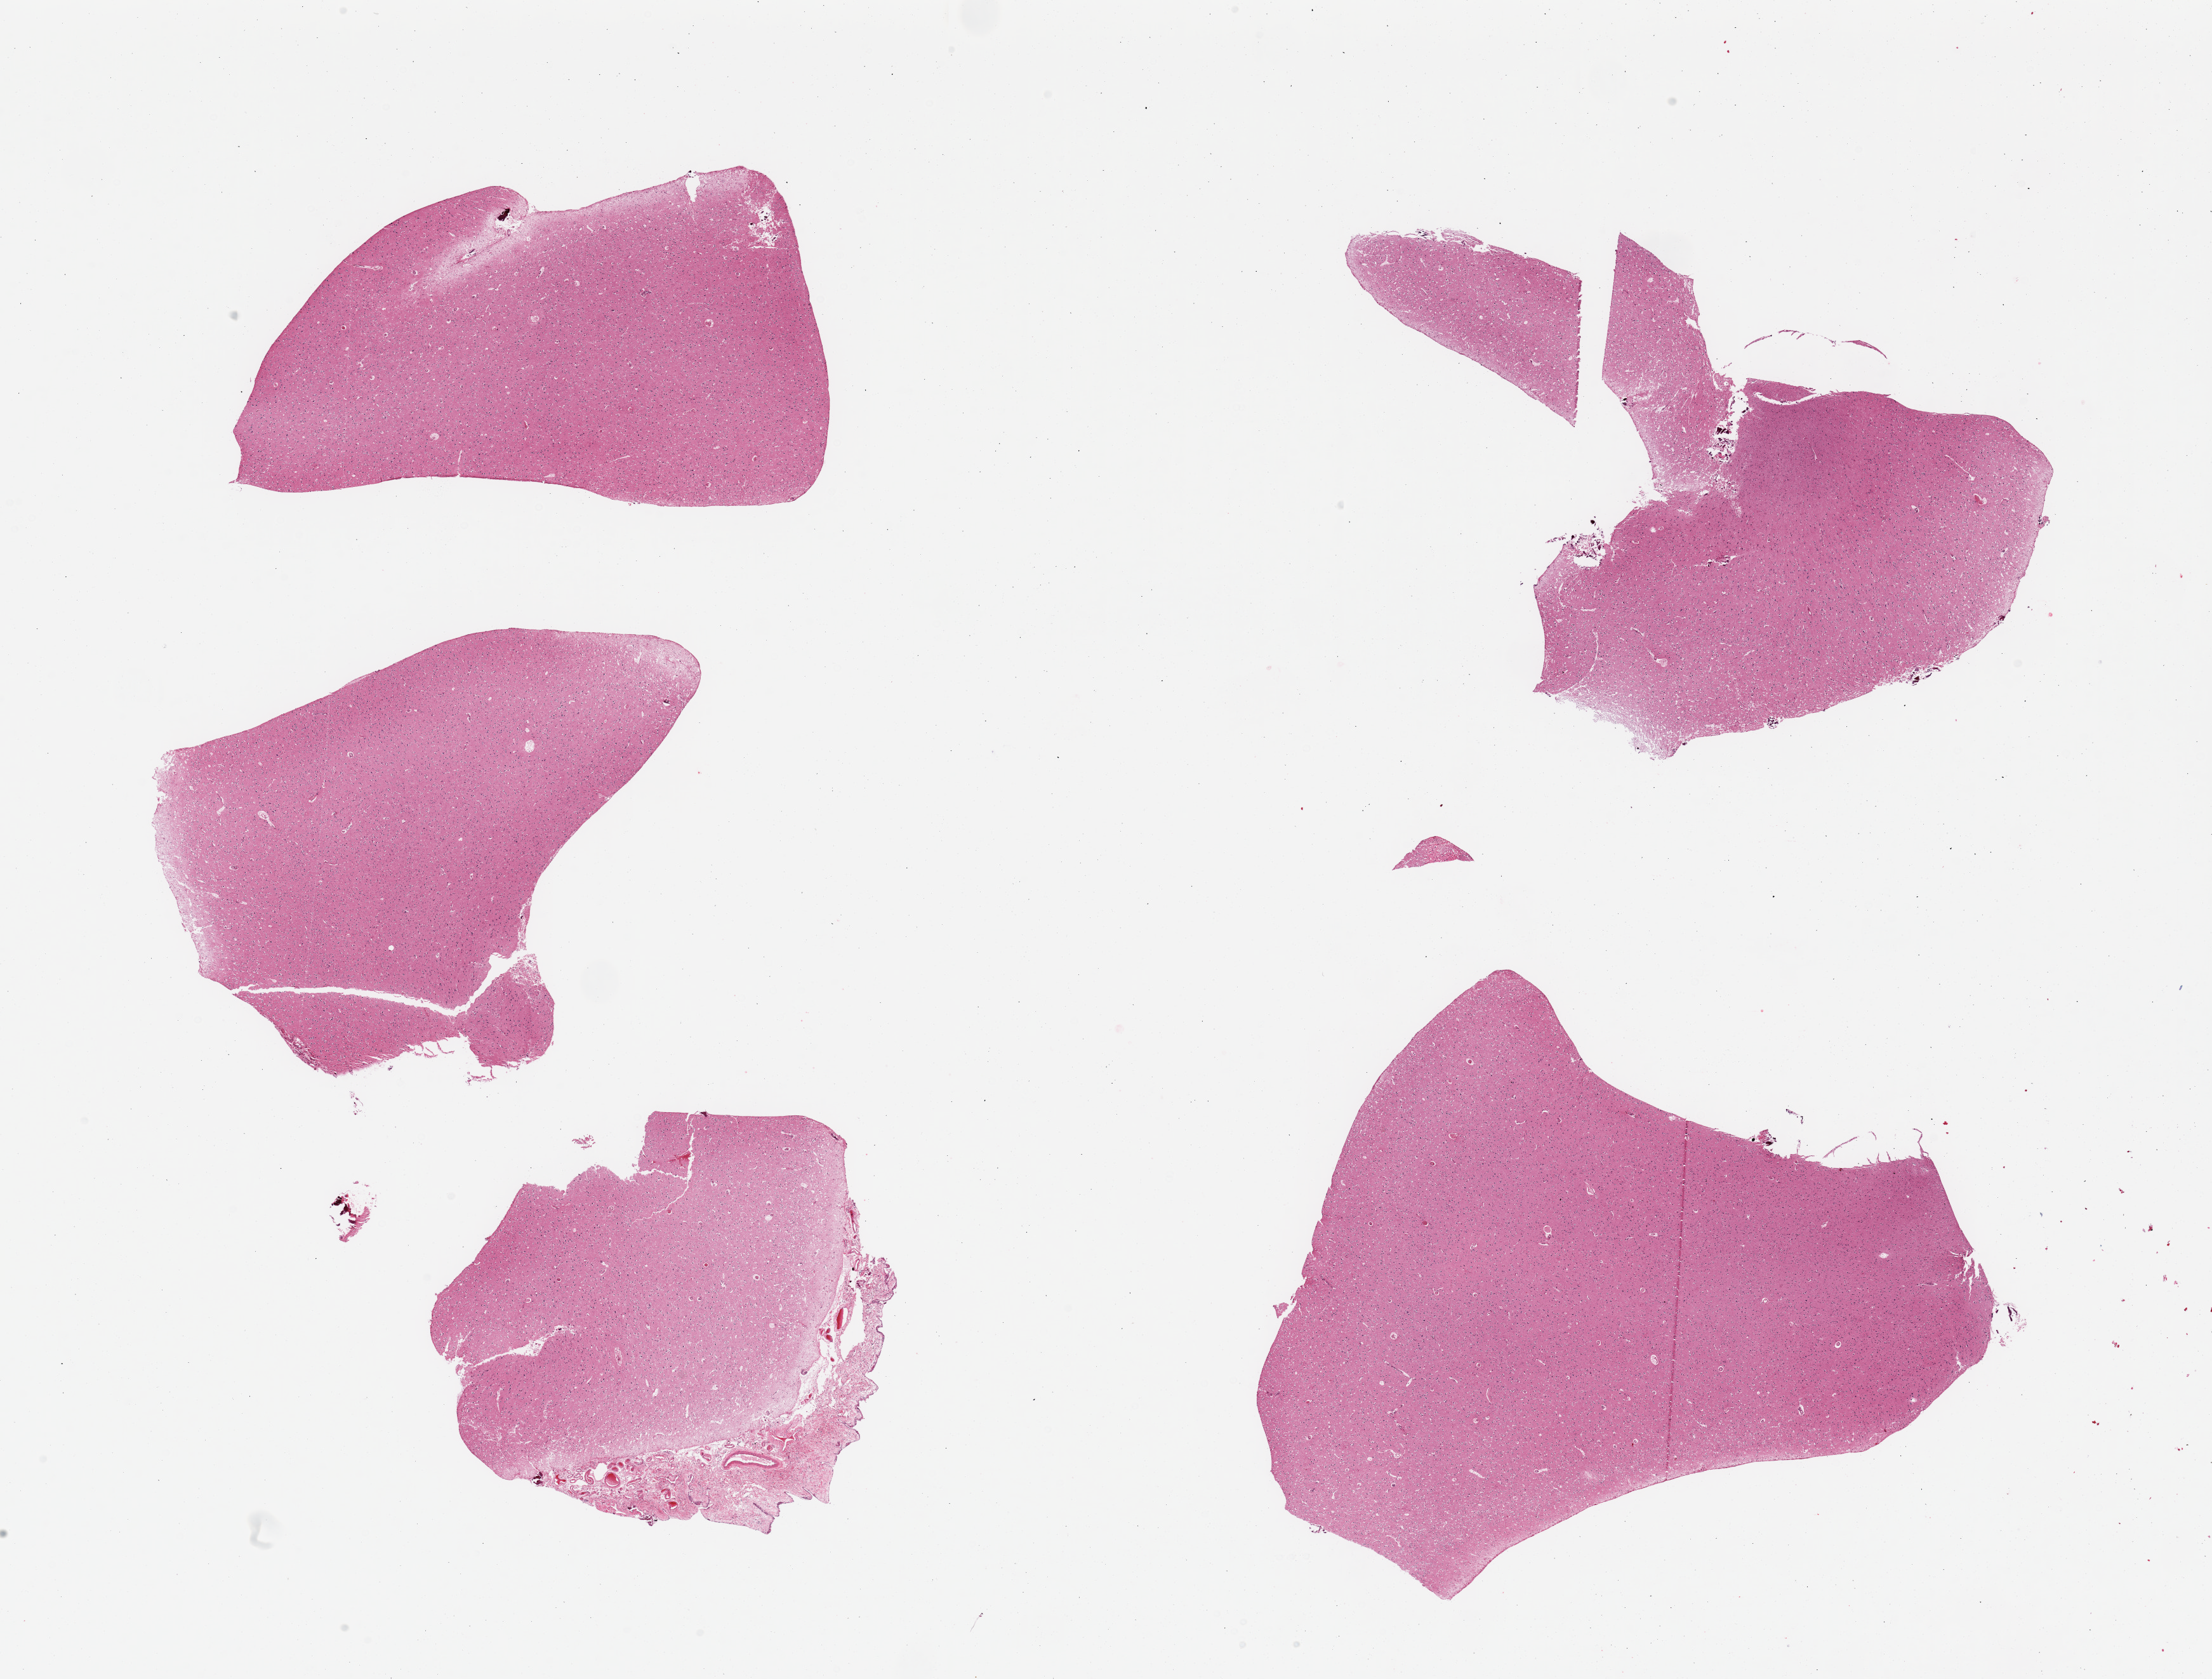
Whole-slide image, hematoxylin and eosin (H&E) stain — low-resolution overview of the scanned area, about 27.6 x 20.9 mm (from a 20x scan). PAXgene-fixed, paraffin-embedded tissue. Sampled site (target tissue): cerebral cortex. Donor tissue sample. Donor sex: male.
Review note (as recorded): 5 pieces, fragmented, no abnormalities.